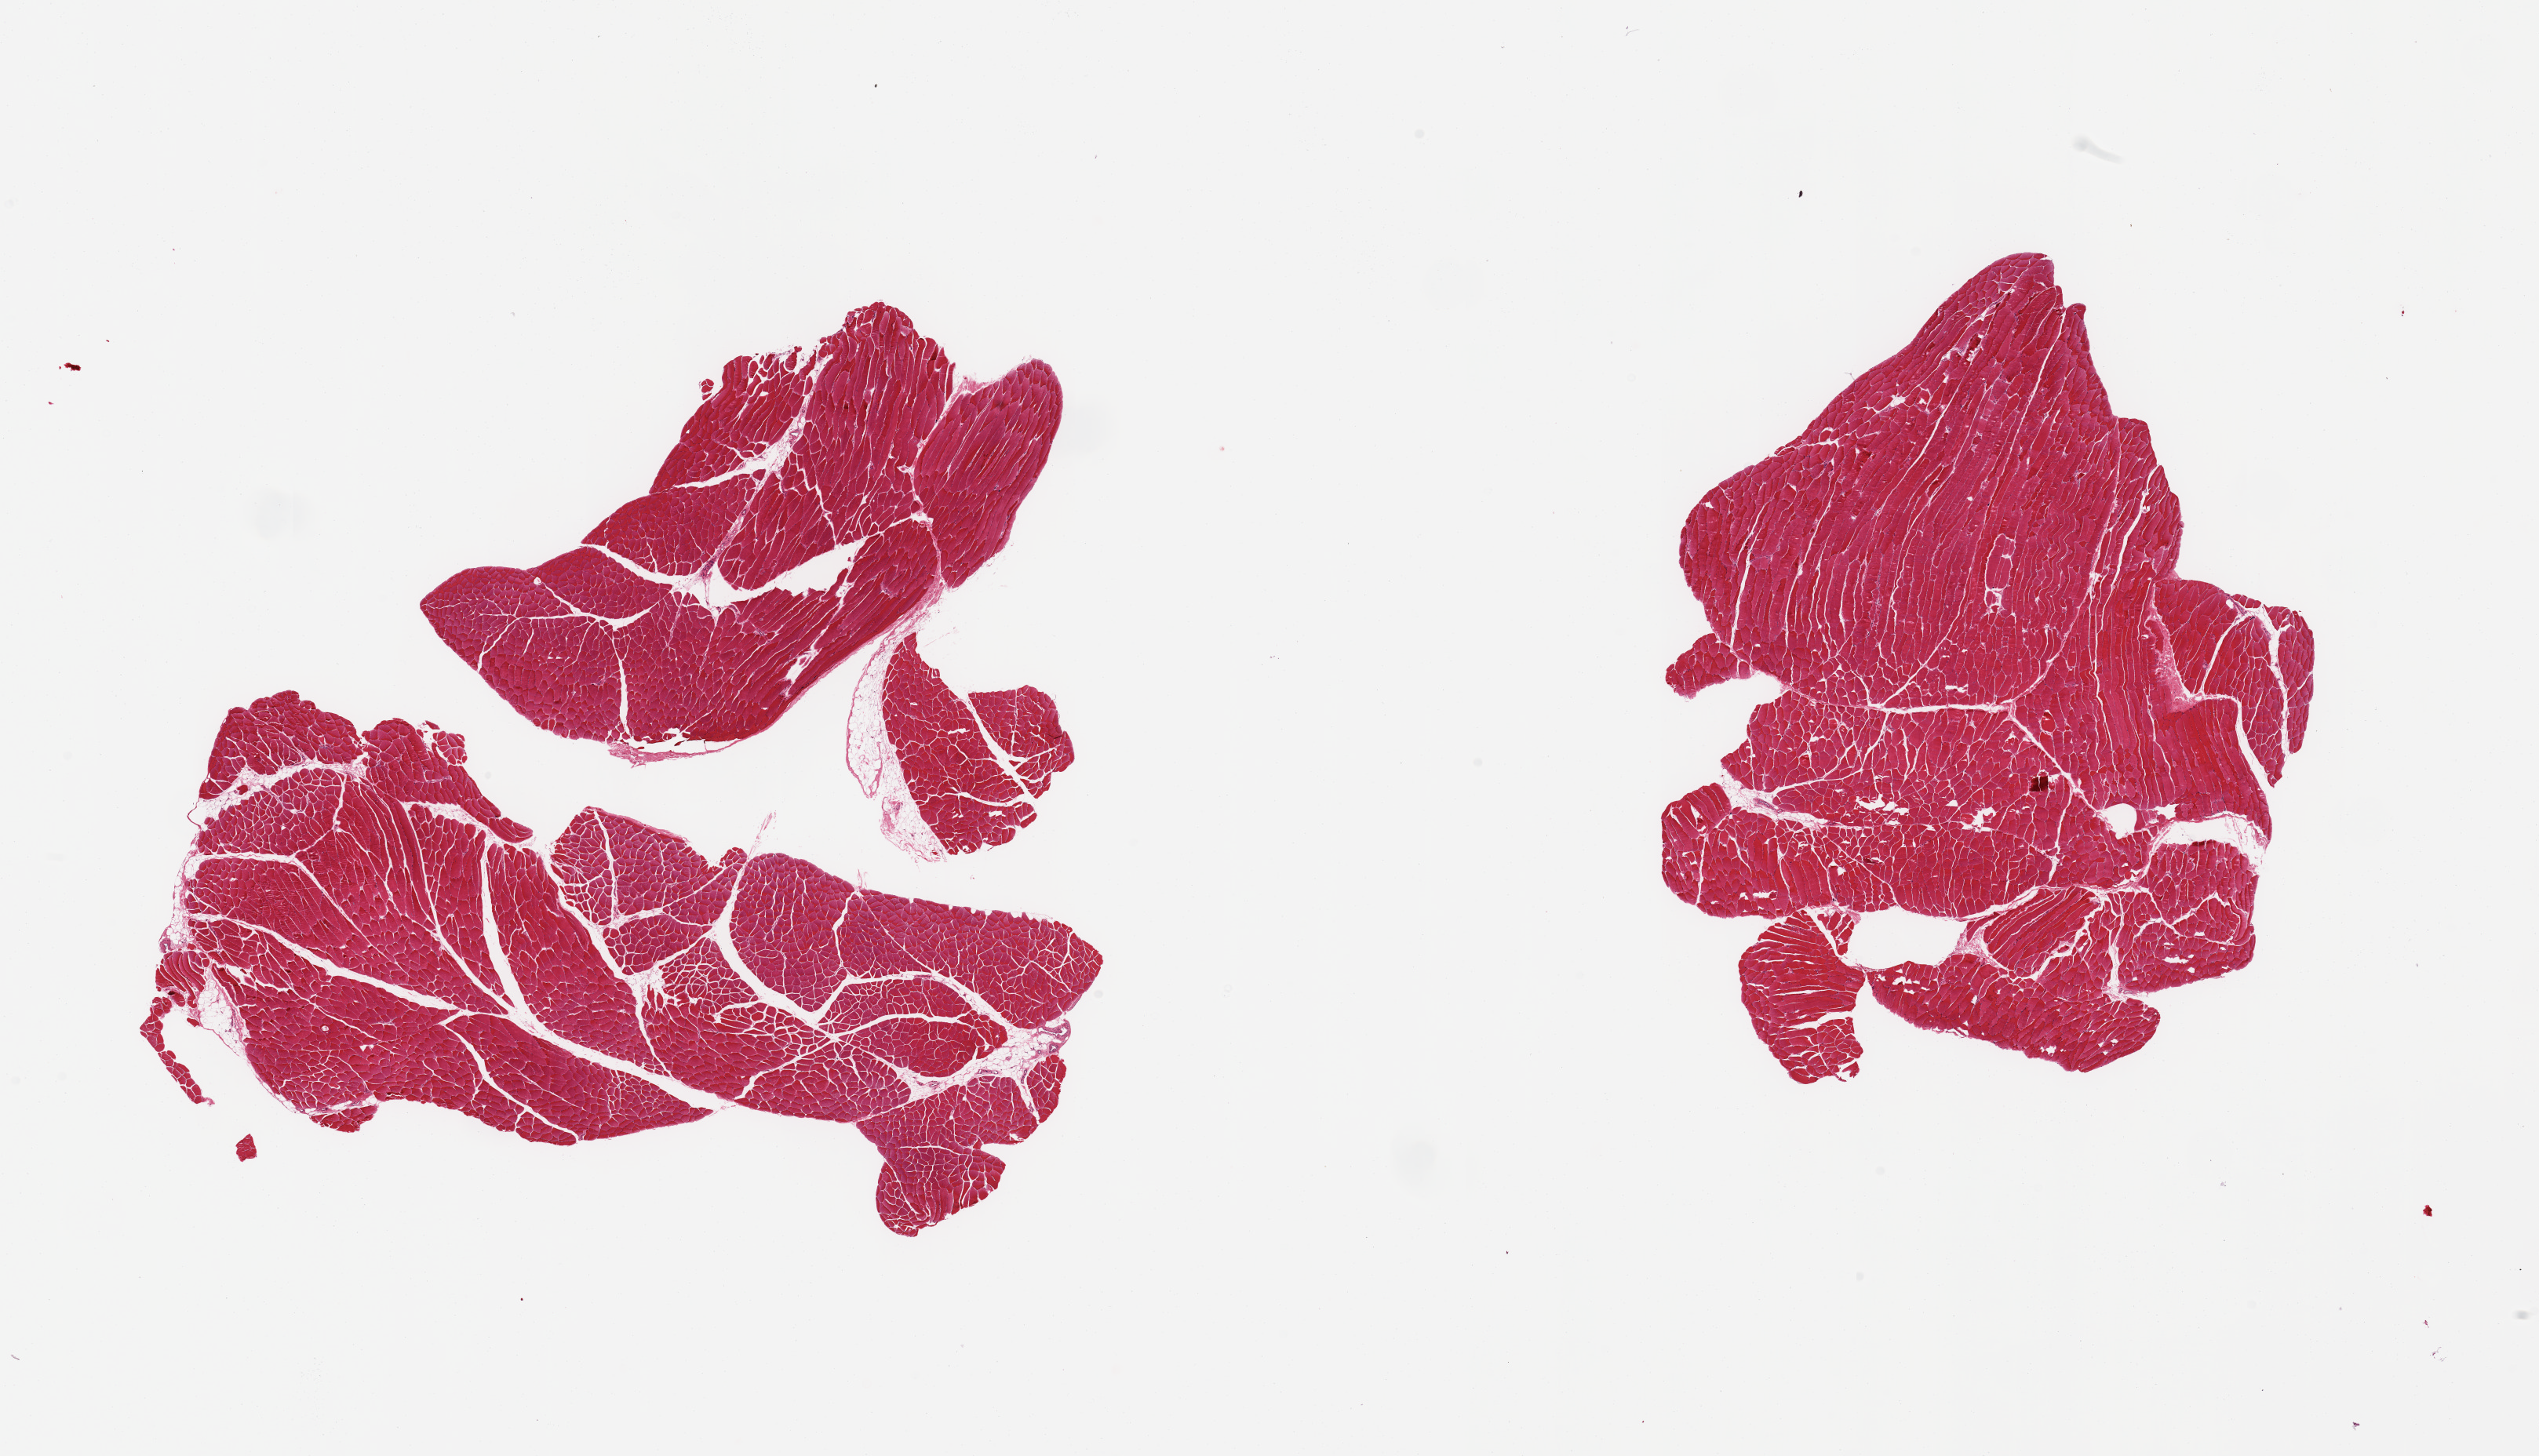
Digitized H&E-stained section — shown as a low-resolution overview of the whole scanned area (about 25.6 x 14.7 mm, from a 20x scan), PAXgene-fixed, paraffin-embedded tissue, target tissue: skeletal muscle, donor tissue sample. Donor: male.
Pathologist's review note for this sample: 2 pieces, ~5% interstitial fat.